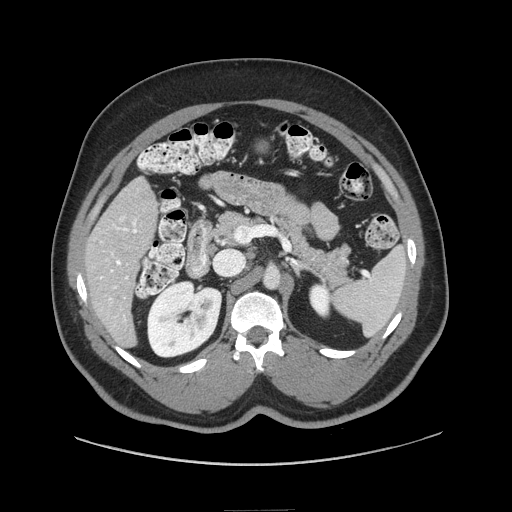
Contrast-enhanced abdominal CT (liver protocol), one axial slice; position 34 of 87 along the scan axis; reconstruction kernel STANDARD; 140 kVp; soft-tissue window (W 400 / L 40 HU); 2.5 mm slice thickness; 512 × 512 image matrix. From the clinical record (not read from this slice): diagnosis: hepatocellular carcinoma (patient treated with transarterial chemoembolisation; whether this scan precedes or follows treatment is not stated here); TNM stage (as recorded): Stage-II; Child-Pugh class: A; tumour nodularity: uninodular.
Structures marked on this image (semi-automatic segmentation, software-assisted and operator-edited):
- liver parenchyma outside the tumour (the mass and vessels are separate outlines, so this box may not span the whole liver): bounding box <84,176,158,346> (left, top, right, bottom; pixels)
- liver vessels: <100,216,137,321>